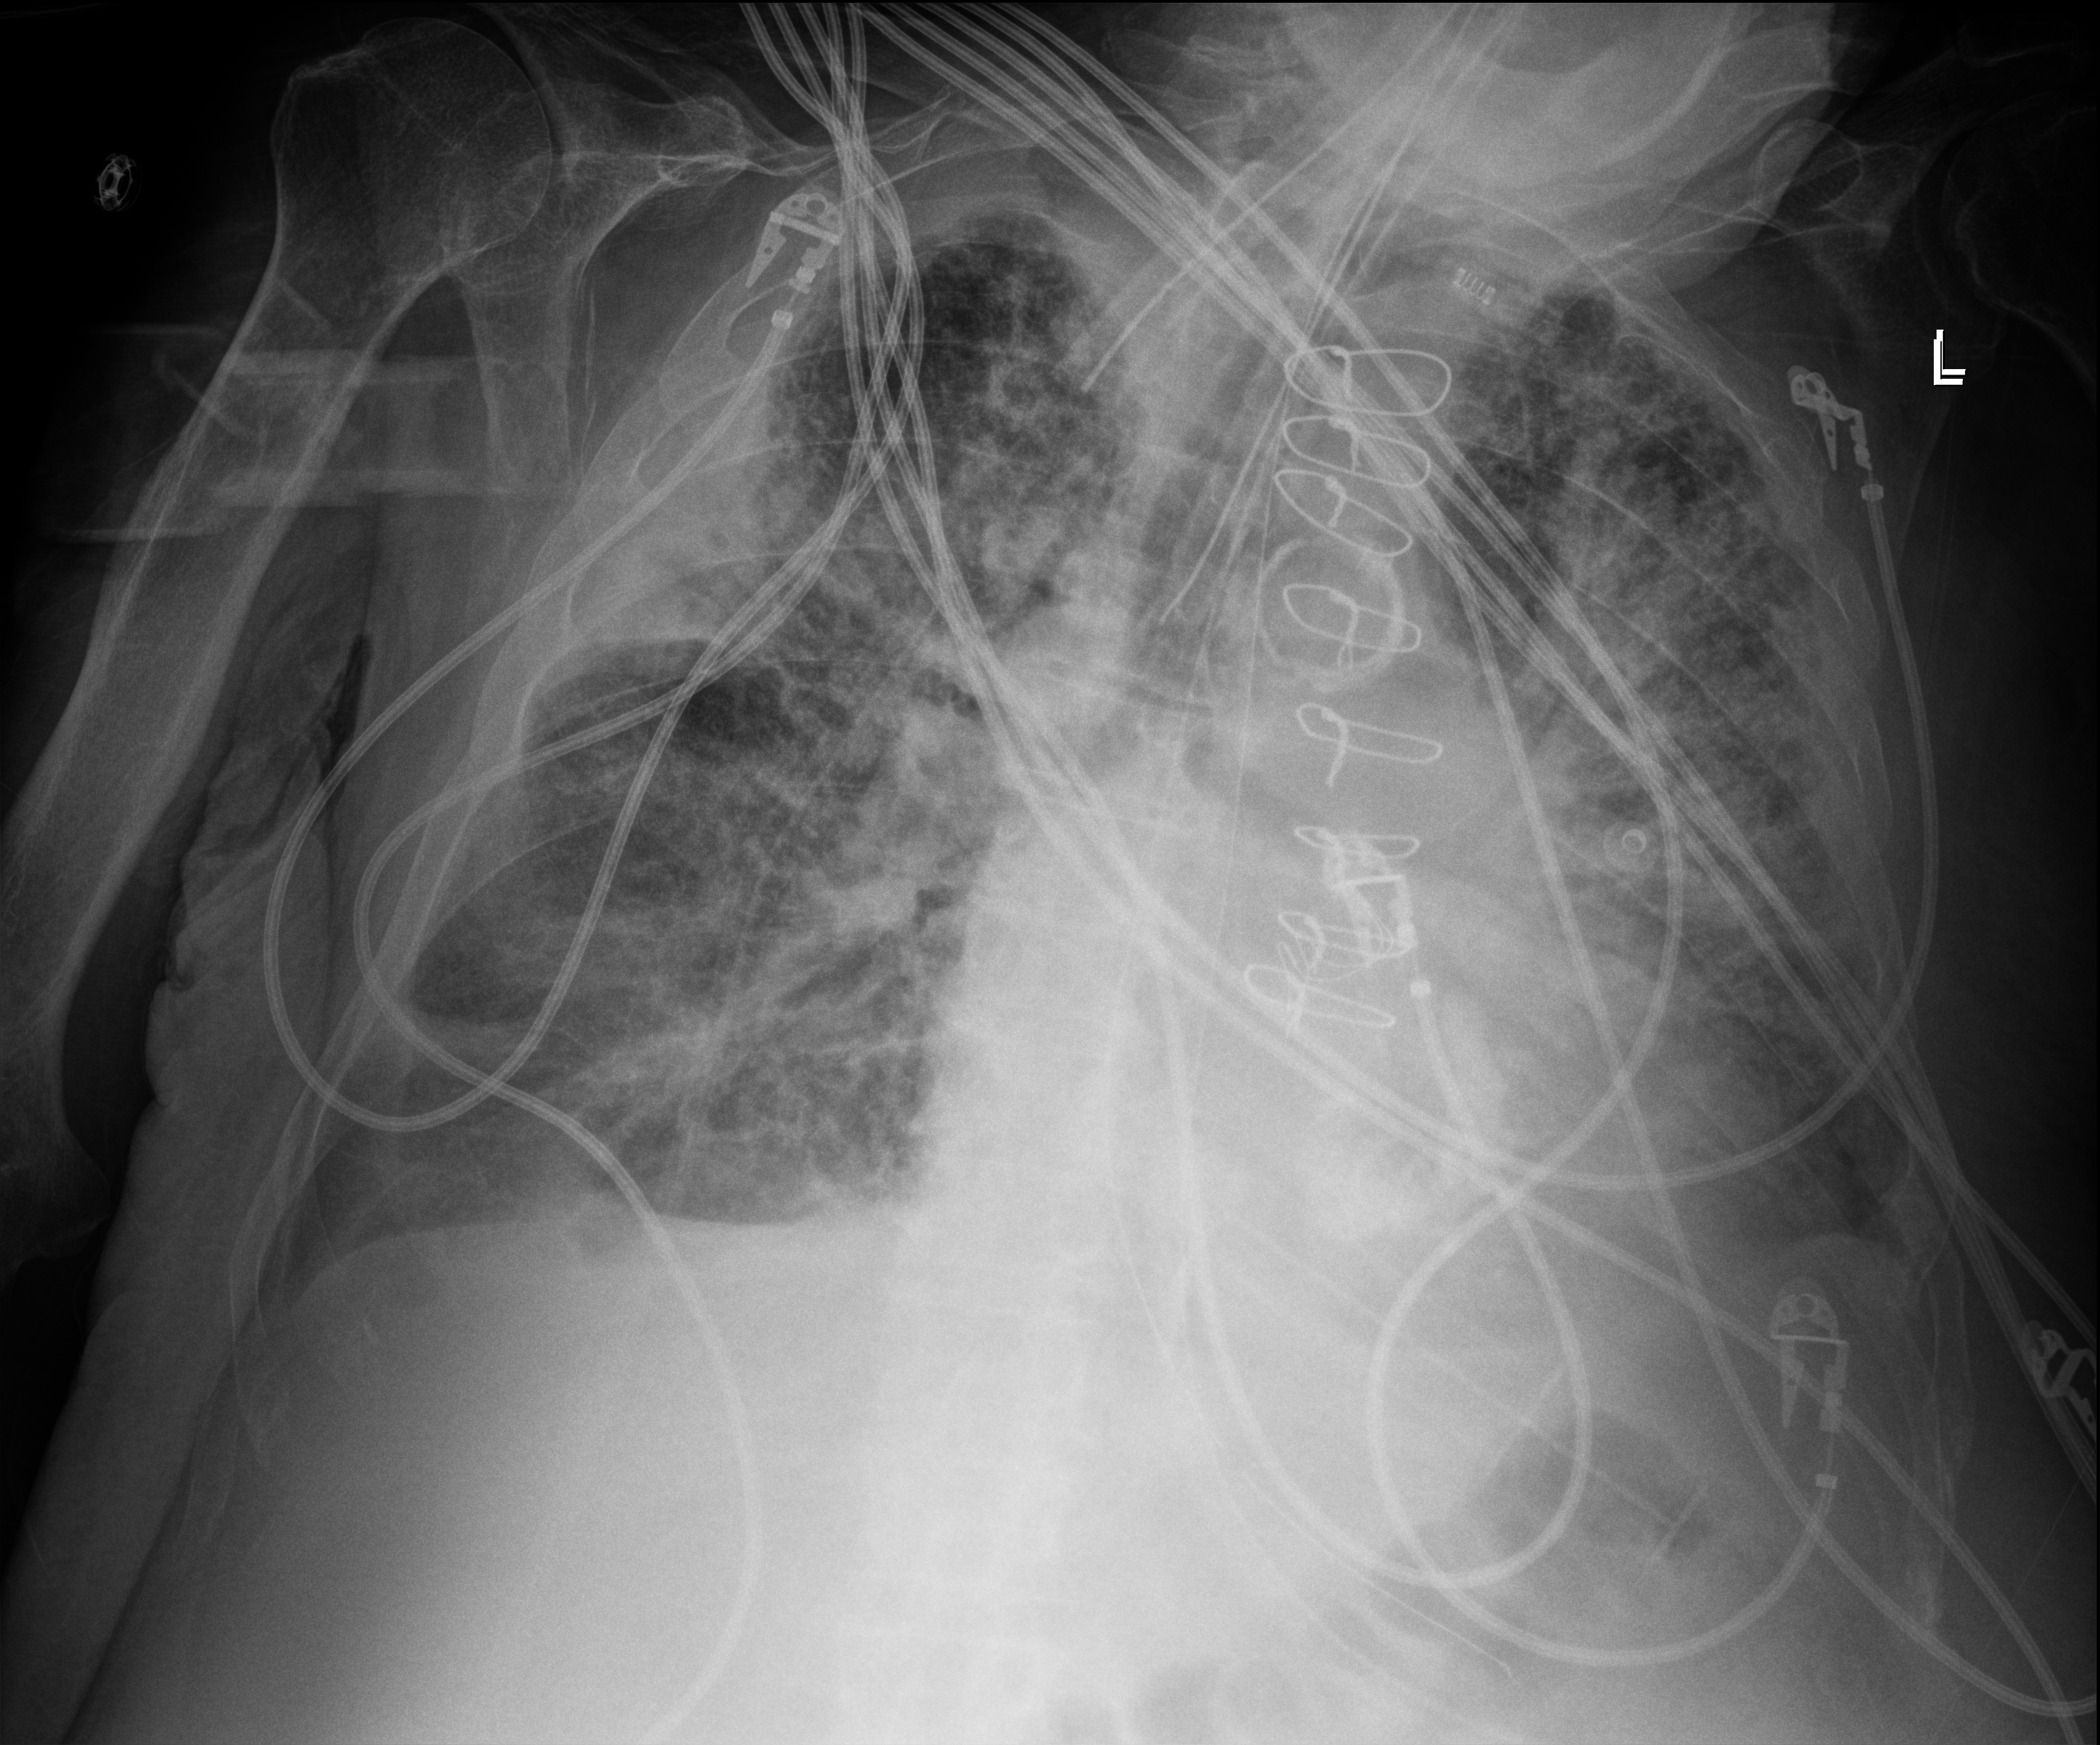
Chest X-ray (portable); anteroposterior (AP) projection. Male patient hospitalised with COVID-19, age 75–90 years.
Hospital-stay facts (about this admission, not read from this image; timing relative to this image not recorded):
- mechanically ventilated during this hospital stay: yes